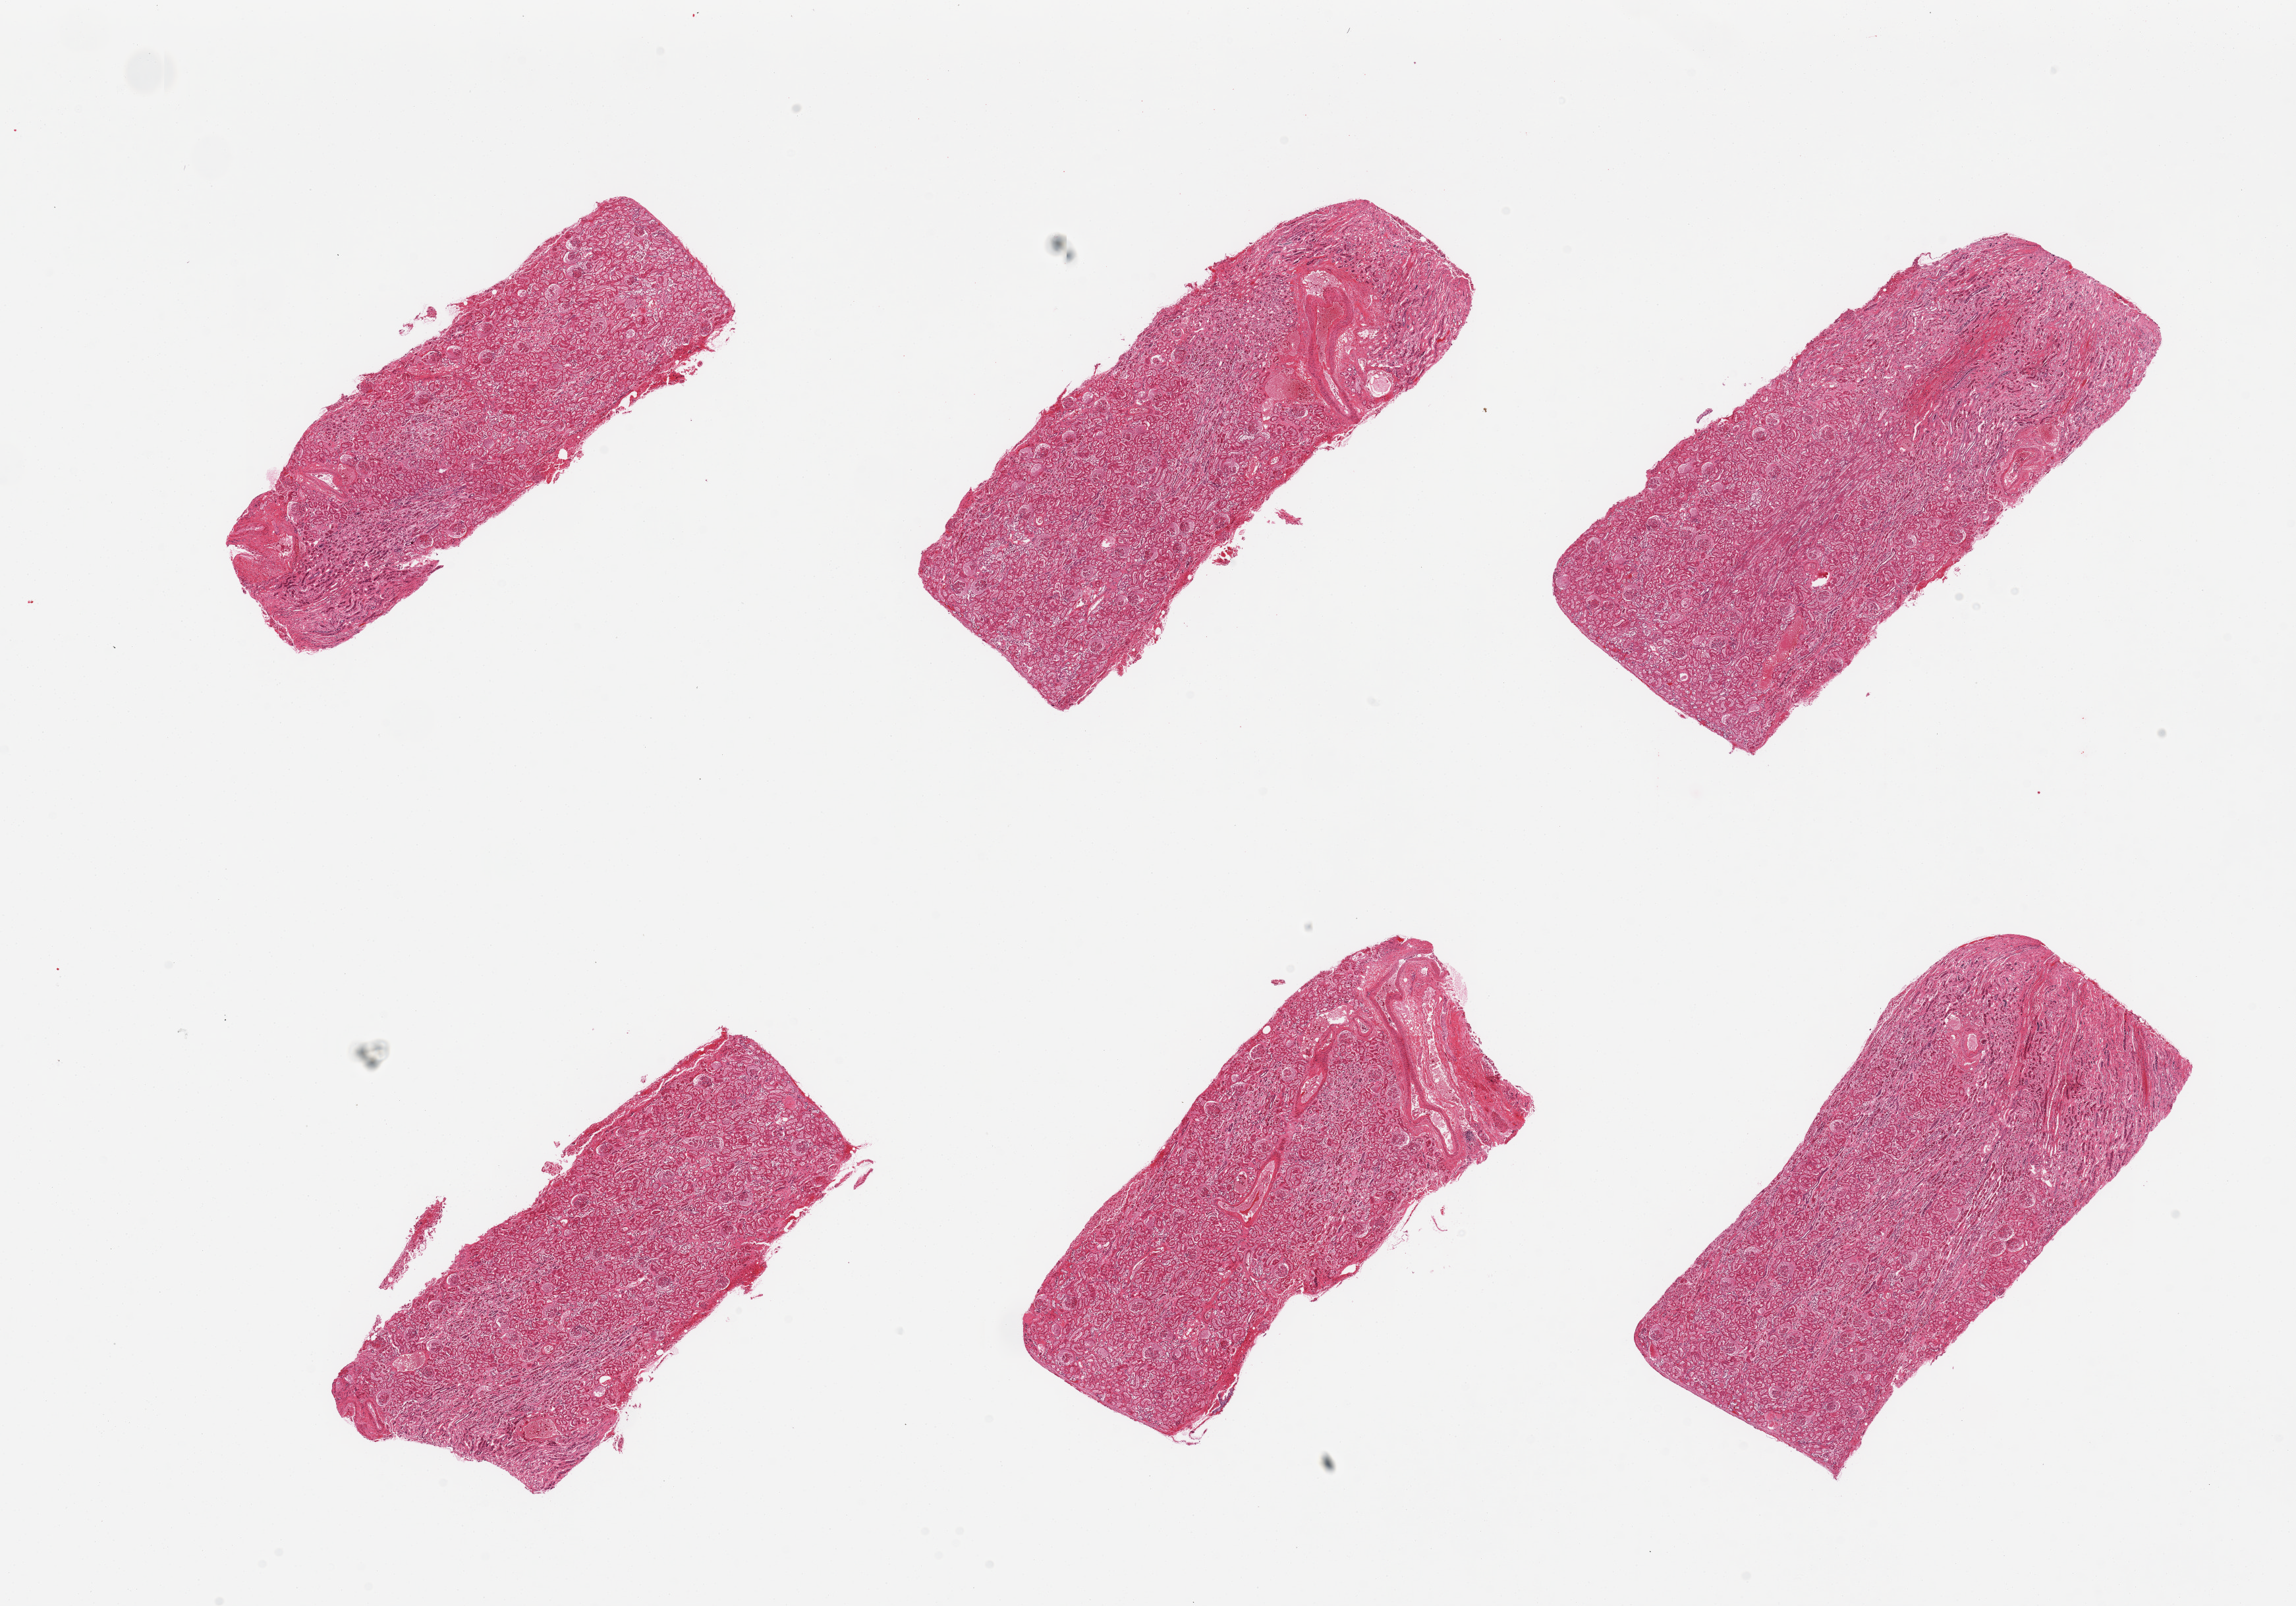
Whole-slide image, haematoxylin and eosin stain, brightfield — a low-resolution overview of the entire scanned area, about 27.6 x 19.3 mm; PAXgene-fixed paraffin-embedded (PFPE) section; section of renal cortex (target tissue); donor tissue sample. Donor: male.
Review note (as recorded): 6 pieces, moderate-severe autolysis; glomeruli seen in all sections.